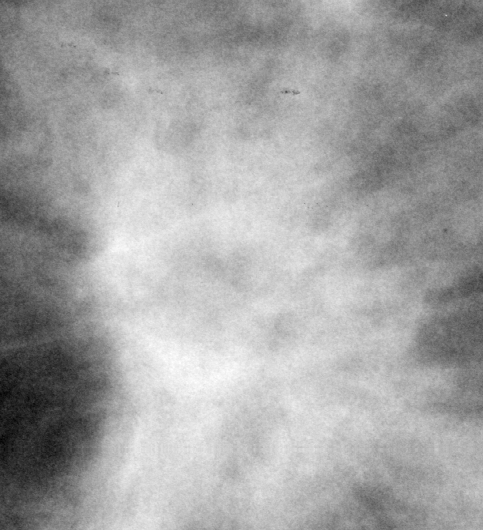
Cropped region of a digitized screen-film mammogram centred on a radiologist-marked abnormality, left breast, CC view.
Mass, shape architectural distortion, margins spiculated; BI-RADS assessment category 5; pathology result (as recorded, not read from the image): malignant.